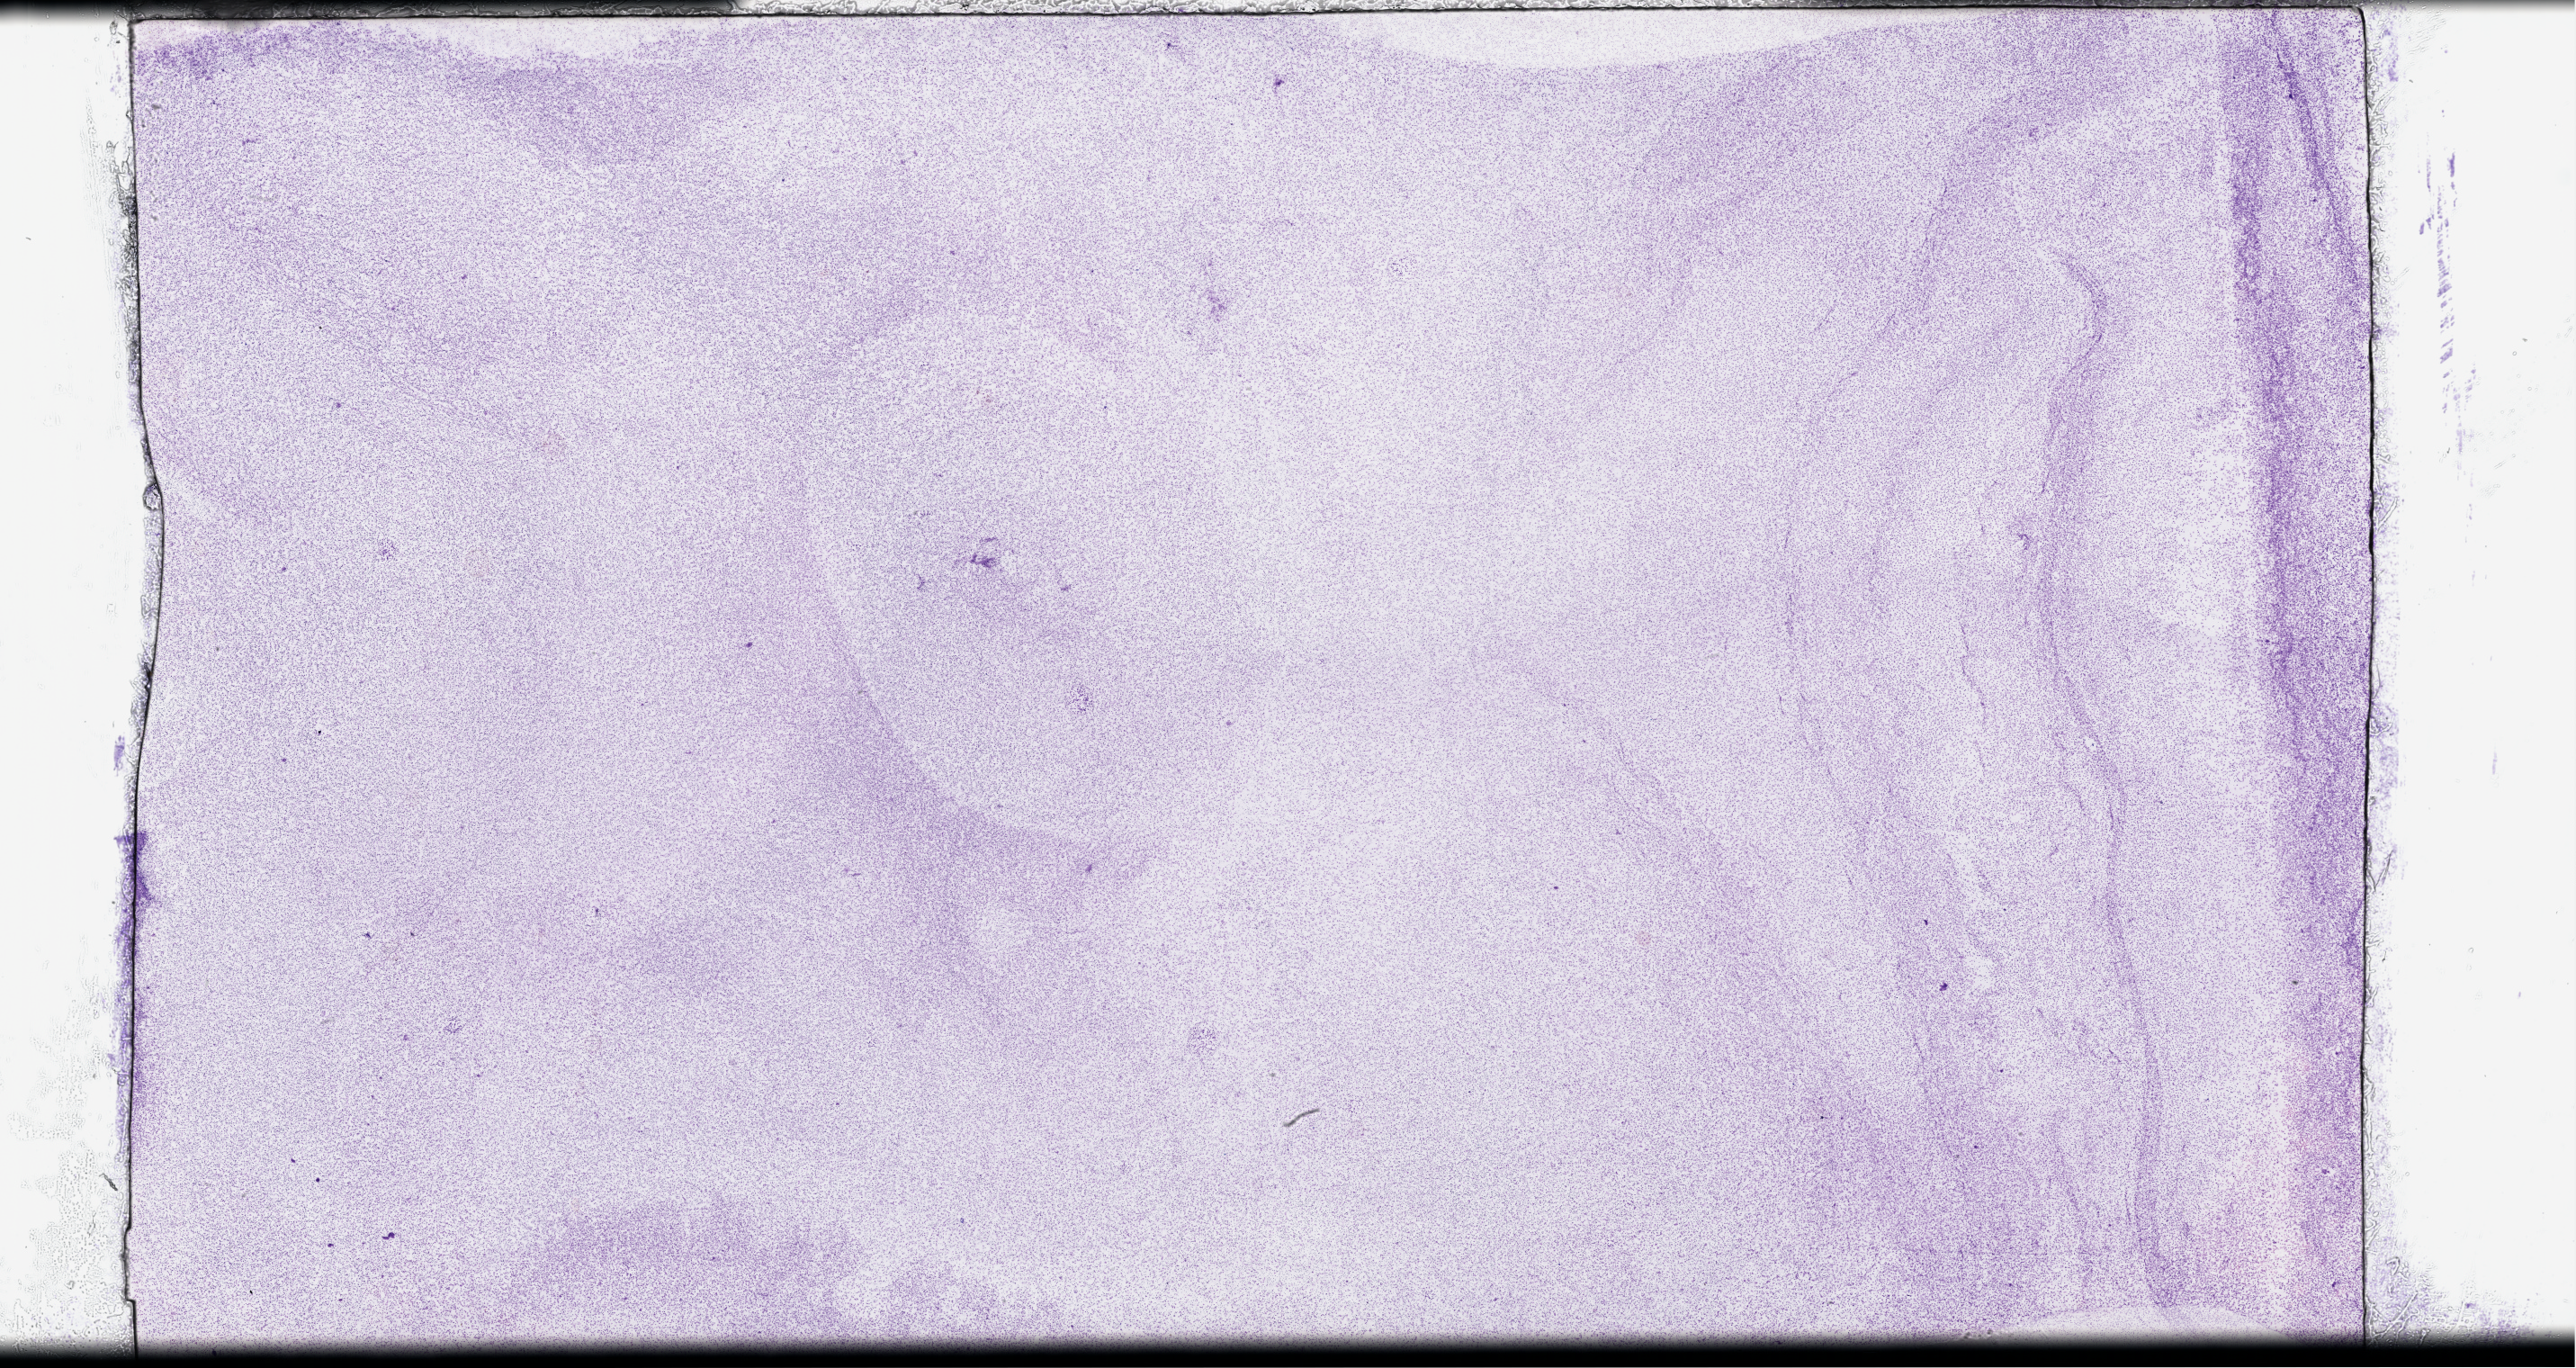
H&E whole-slide image, whole scanned area (about 46.2 x 24.5 mm) shown as a low-resolution overview, peripheral blood (leukaemic) sample. 47-year-old female patient.
WHO classification: AML with maturation. FAB classification: M2. Diagnosis: Acute Myeloid Leukemia.